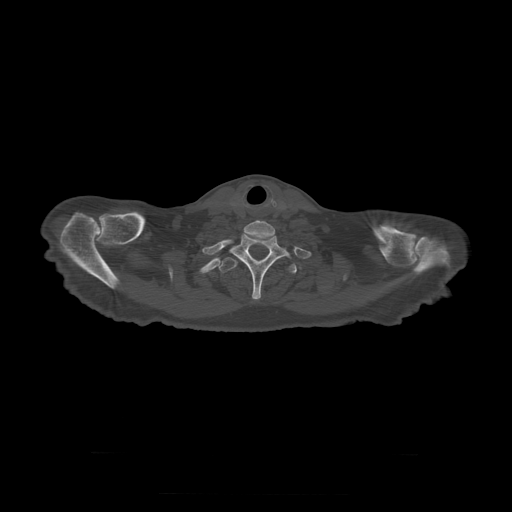
CT including the spine, one axial slice. 120 kVp. Bone window (W 1800 / L 400 HU). 1.25 mm slice thickness. 512 × 512 image matrix. Patient age 73 years. Case-level facts recorded for this patient, not image findings: primary cancer: prostate.
Annotated regions visible in this slice (semi-automatically segmented with operator editing):
- T1 vertebra: bounding box [x1, y1, x2, y2] px = [231, 233, 289, 300]
- T2 vertebra: [219, 258, 297, 275]